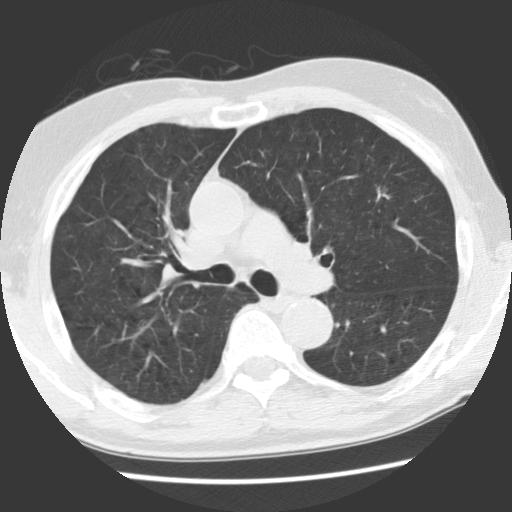
Low-dose screening chest CT, axial slice; baseline annual screen; lung window (W 1500 / L -600 HU); slice 82 of 131 in the series; 512 × 512 image matrix. Male, age 70 years at enrolment.
• Lesion marked by an expert reader, bounding box (x1, y1, x2, y2) in pixels: (351, 178, 402, 223).
• The screening reader recorded 2 non-calcified nodules or masses ≥4 mm on this exam; which of them this box marks is not recorded.
• Later outcome: lung cancer diagnosed 879 days after this screen (after the third annual screen) — adenocarcinoma, NOS, left upper lobe, moderately differentiated (G2), stage IIIA (AJCC 6th edition), 17 mm at pathology.